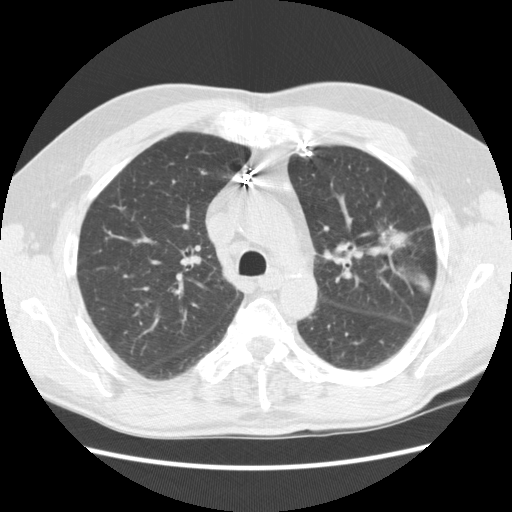
Chest CT (low-dose screening protocol), one axial image. First (baseline) screen. Lung window (W 1500 / L -600 HU). 512 × 512 image matrix. Male participant, aged 72 years at enrolment. Former smoker at enrolment.
Expert reader's lesion annotation, bounding box <361,213,427,260> (left, top, right, bottom; pixels). The exam's reader record, not a measurement of the box and not confirmed to be the same lesion: non-calcified nodule or mass ≥4 mm, left upper lobe, 25 × 18 mm, spiculated (stellate) margins, soft tissue attenuation.